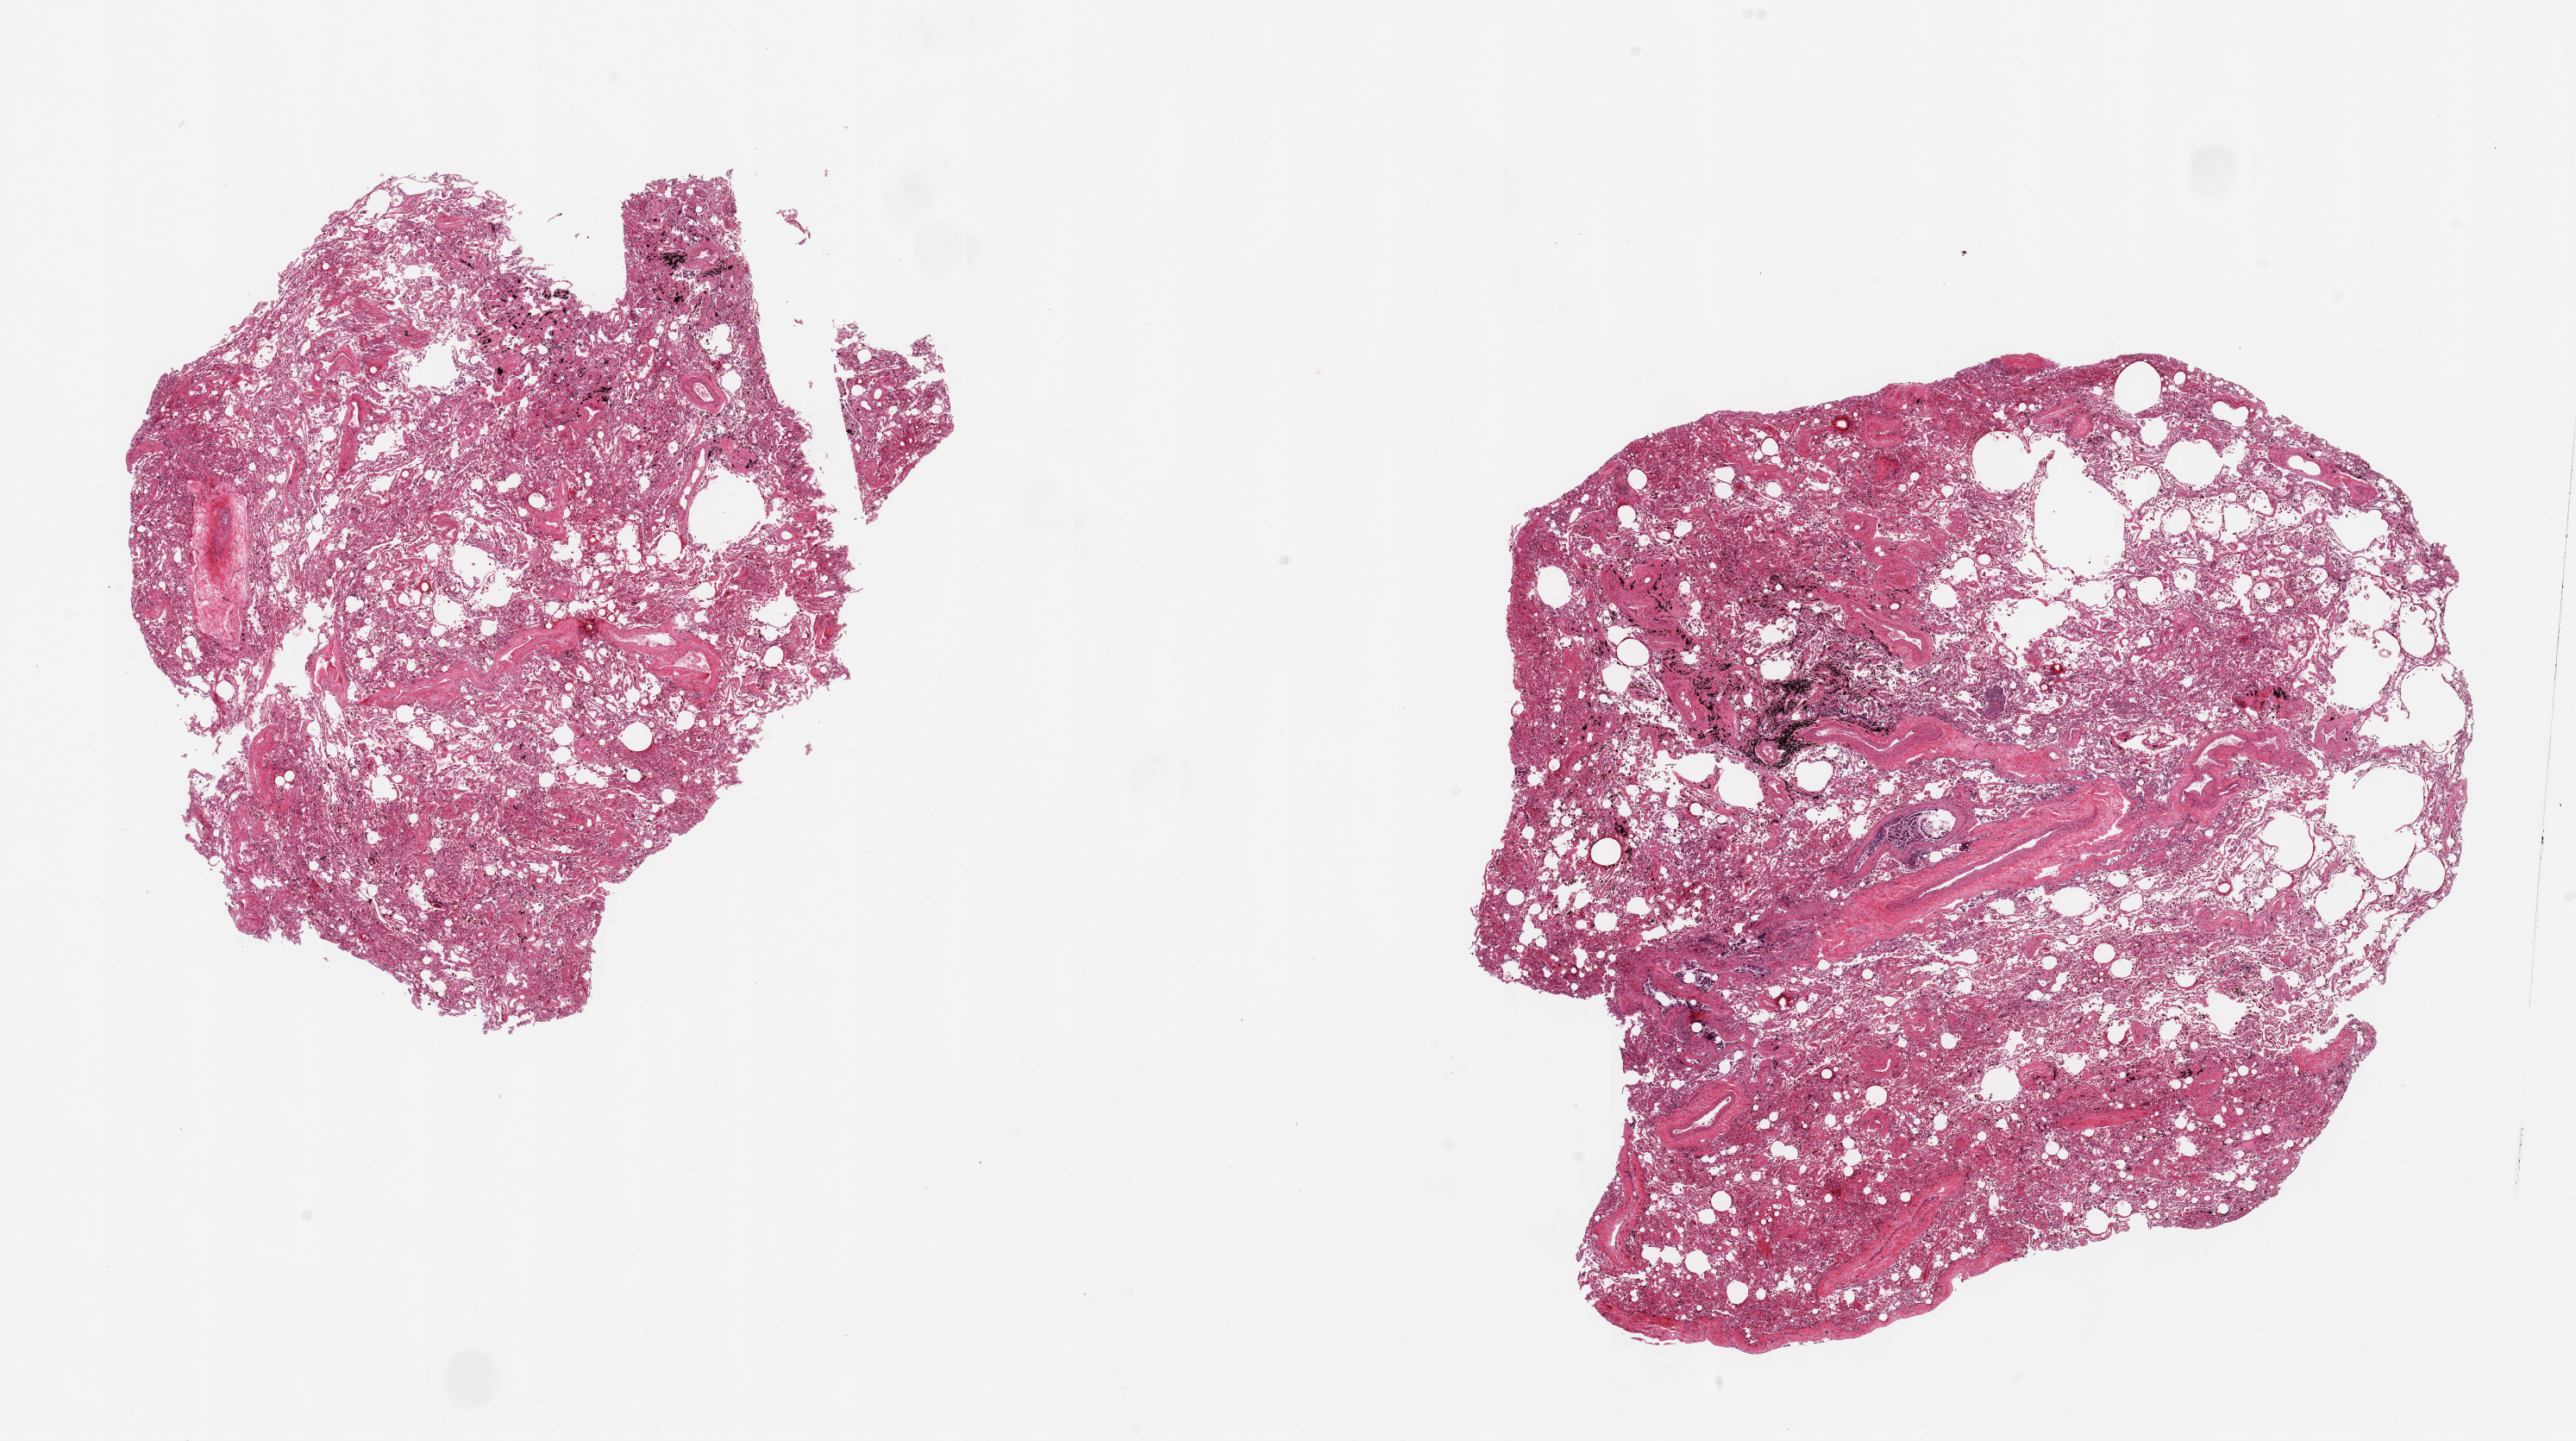
Whole-slide image, haematoxylin and eosin stain, shown as a low-resolution overview of the whole scanned area (about 23.6 x 13.2 mm). PAXgene-fixed, paraffin-embedded tissue. Target tissue: lung. Tissue donor sample.
- reviewer comment on this tissue sample: 2 pieces, mild chronic congestion